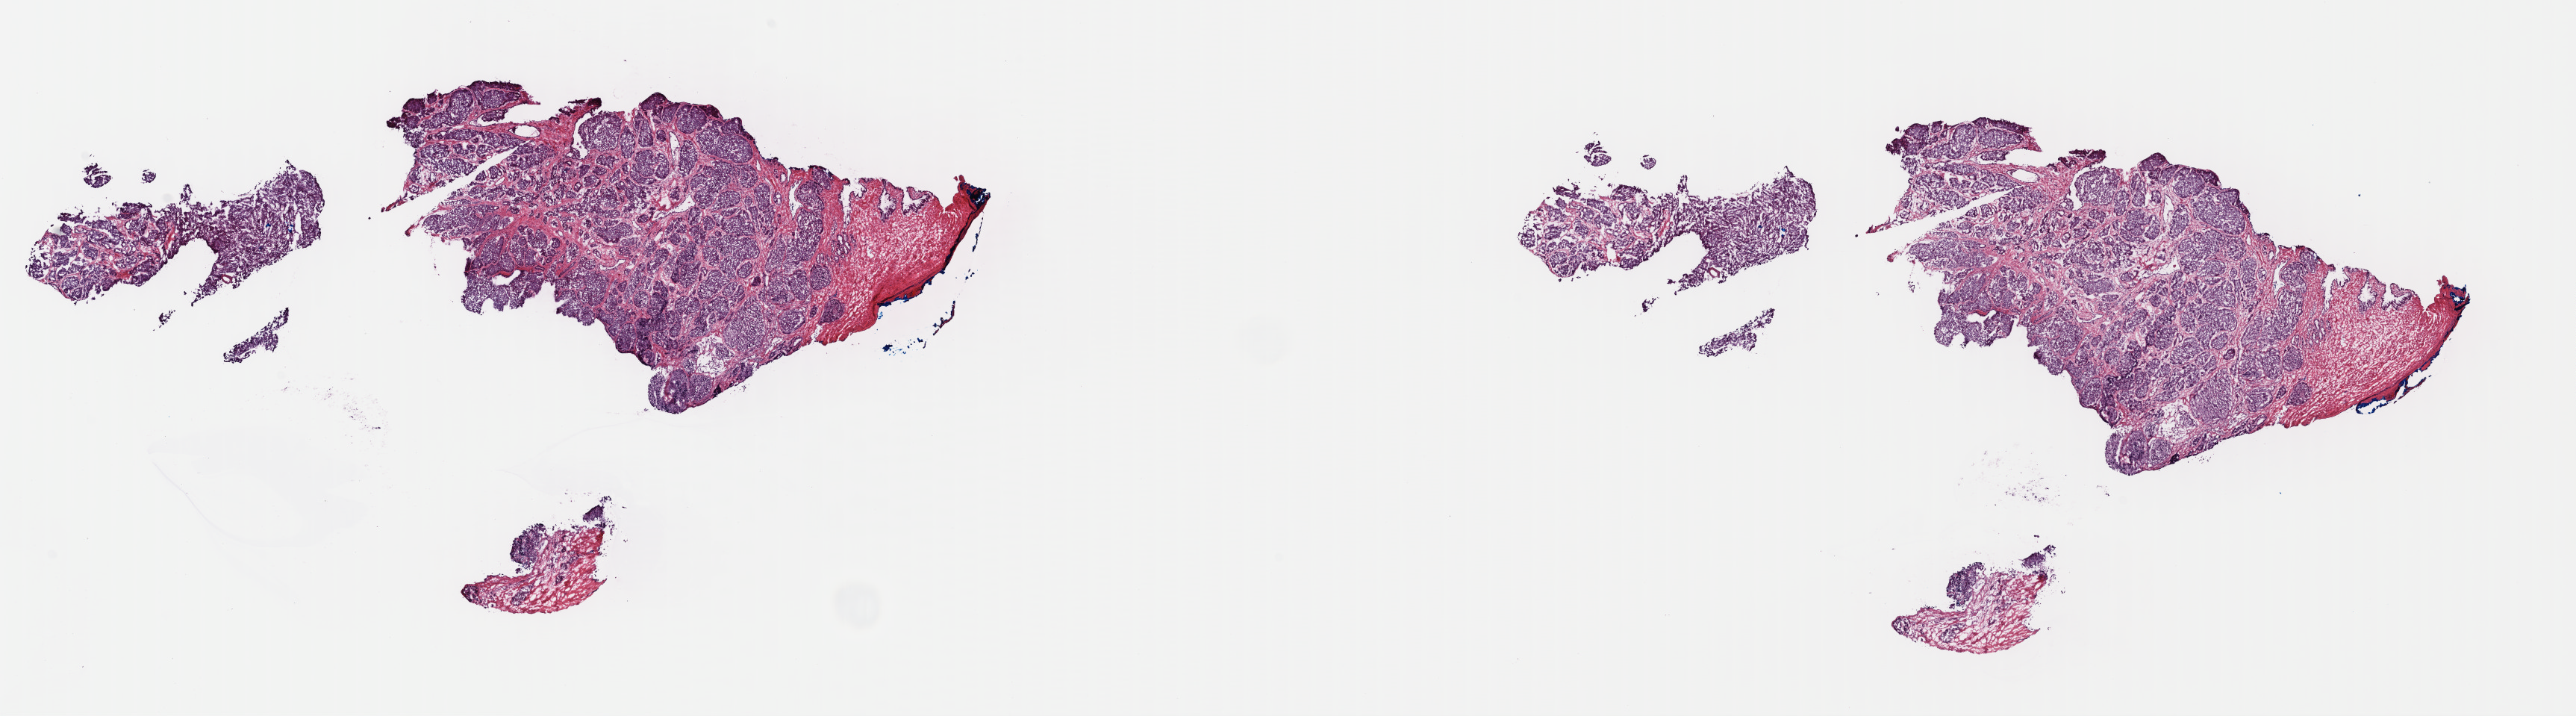
Digitized H&E-stained tissue section (whole slide) — whole scanned area (about 27.1 x 7.5 mm) shown as a low-resolution overview, frozen section, prostate, primary tumour sample. Male, age 62 years at initial diagnosis. Gleason score: 7 (4+3). Slide review estimates, as recorded: tumour cells 80%, tumour nuclei 80%, normal cells 0%, stromal cells 20%, necrosis 0%. Infiltration values recorded for this section: lymphocyte infiltration 40%, monocyte infiltration 20%, neutrophil infiltration 20%.
• pathologic diagnosis: Adenocarcinoma, NOS
• lymph nodes positive (case pathology): 0 of 9 examined